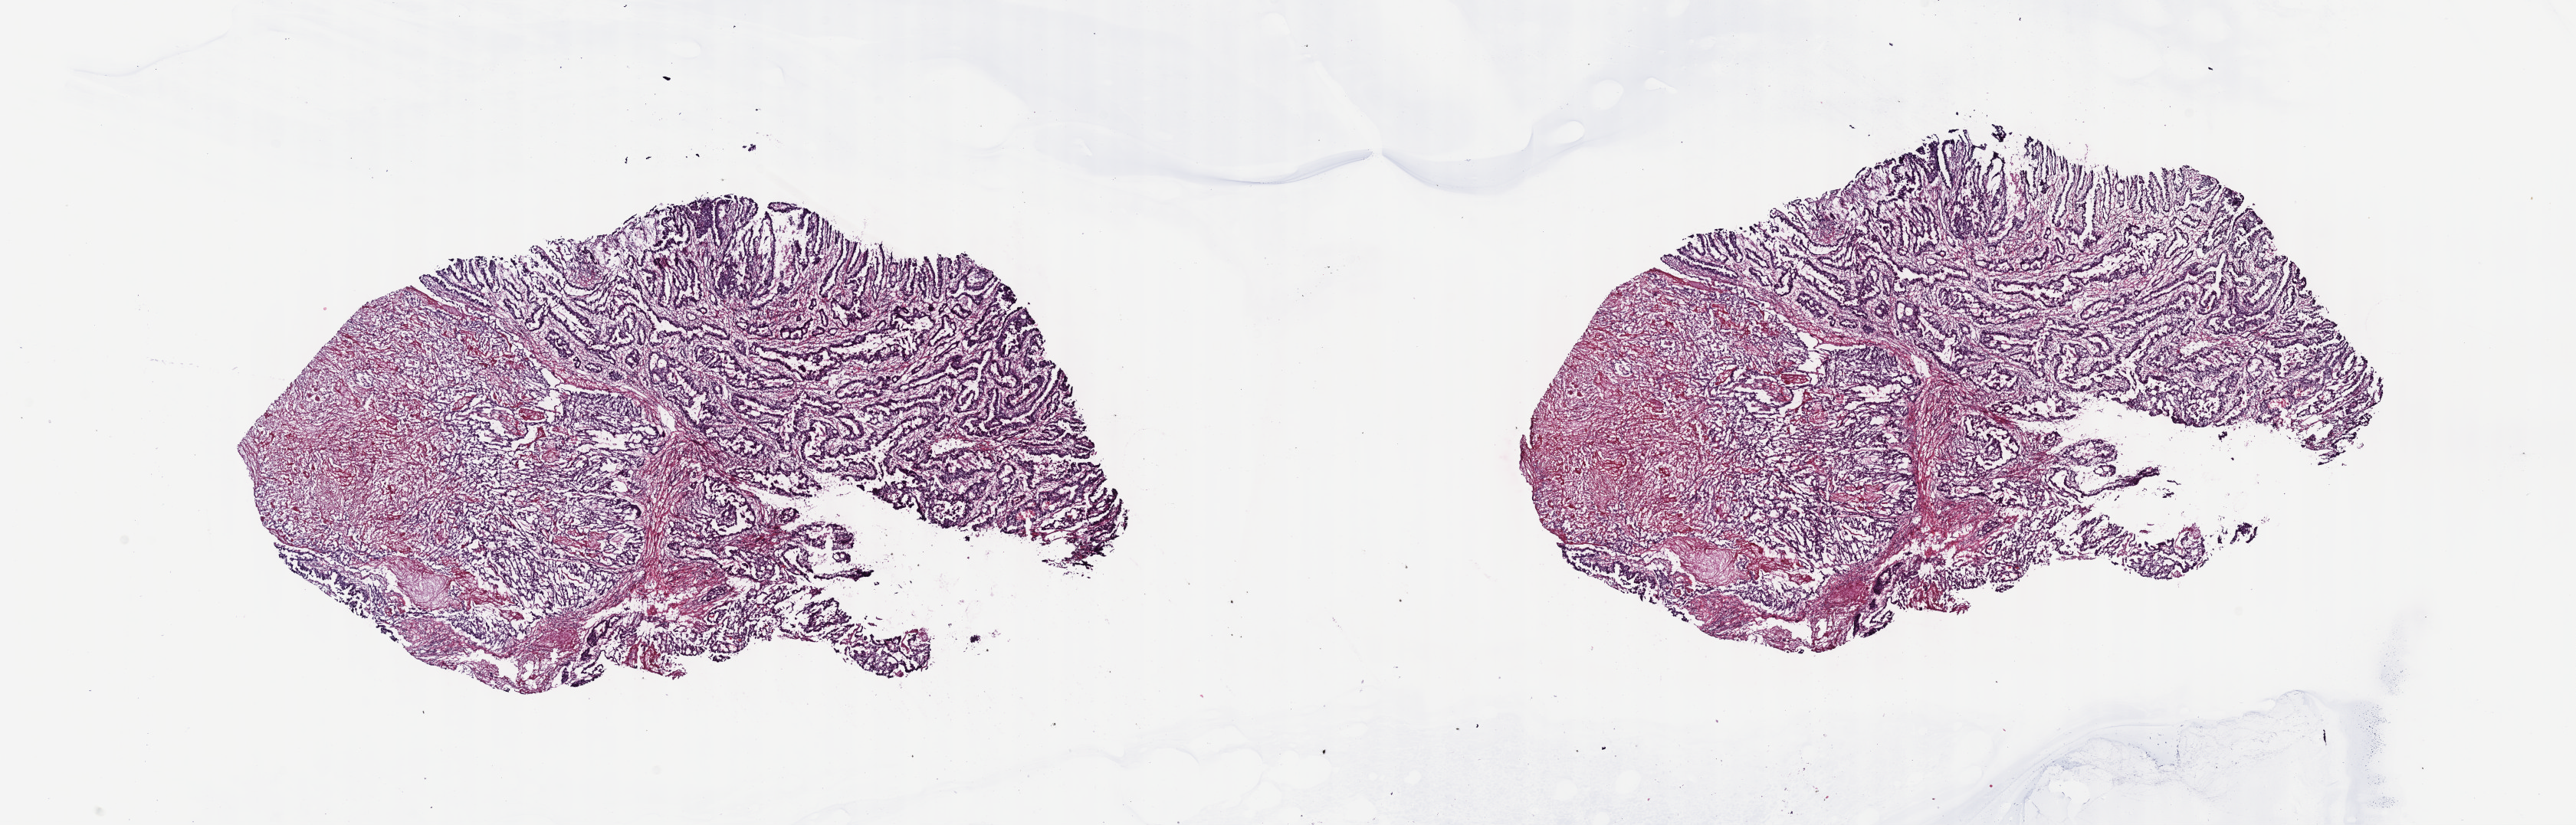
Digitized H&E tissue section (whole slide), low-resolution overview of the scanned area, about 27.2 x 8.7 mm, frozen section from the top of the tissue portion, sample: primary tumour, stomach. Patient: male, age at initial diagnosis 48 years.
Pathologic diagnosis: Adenocarcinoma, intestinal type (gastric antrum).